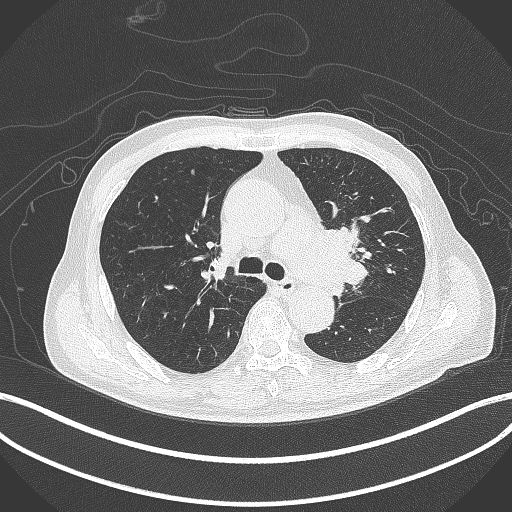
Chest CT, one axial slice. Reconstruction kernel B70f. Lung window (W 1500 / L -600 HU). 512 × 512 image matrix, field of view 400 × 400 mm. Male patient, age 77 years. Case-level facts recorded for this patient, not image findings: clinical TNM (as recorded): T3 N1 M0.
Structures marked on this image (rectangle marked by the reading radiologist):
- lung tumour (recorded histology: adenocarcinoma): bounding box (x1, y1, x2, y2) in pixels: (313, 222, 368, 297)